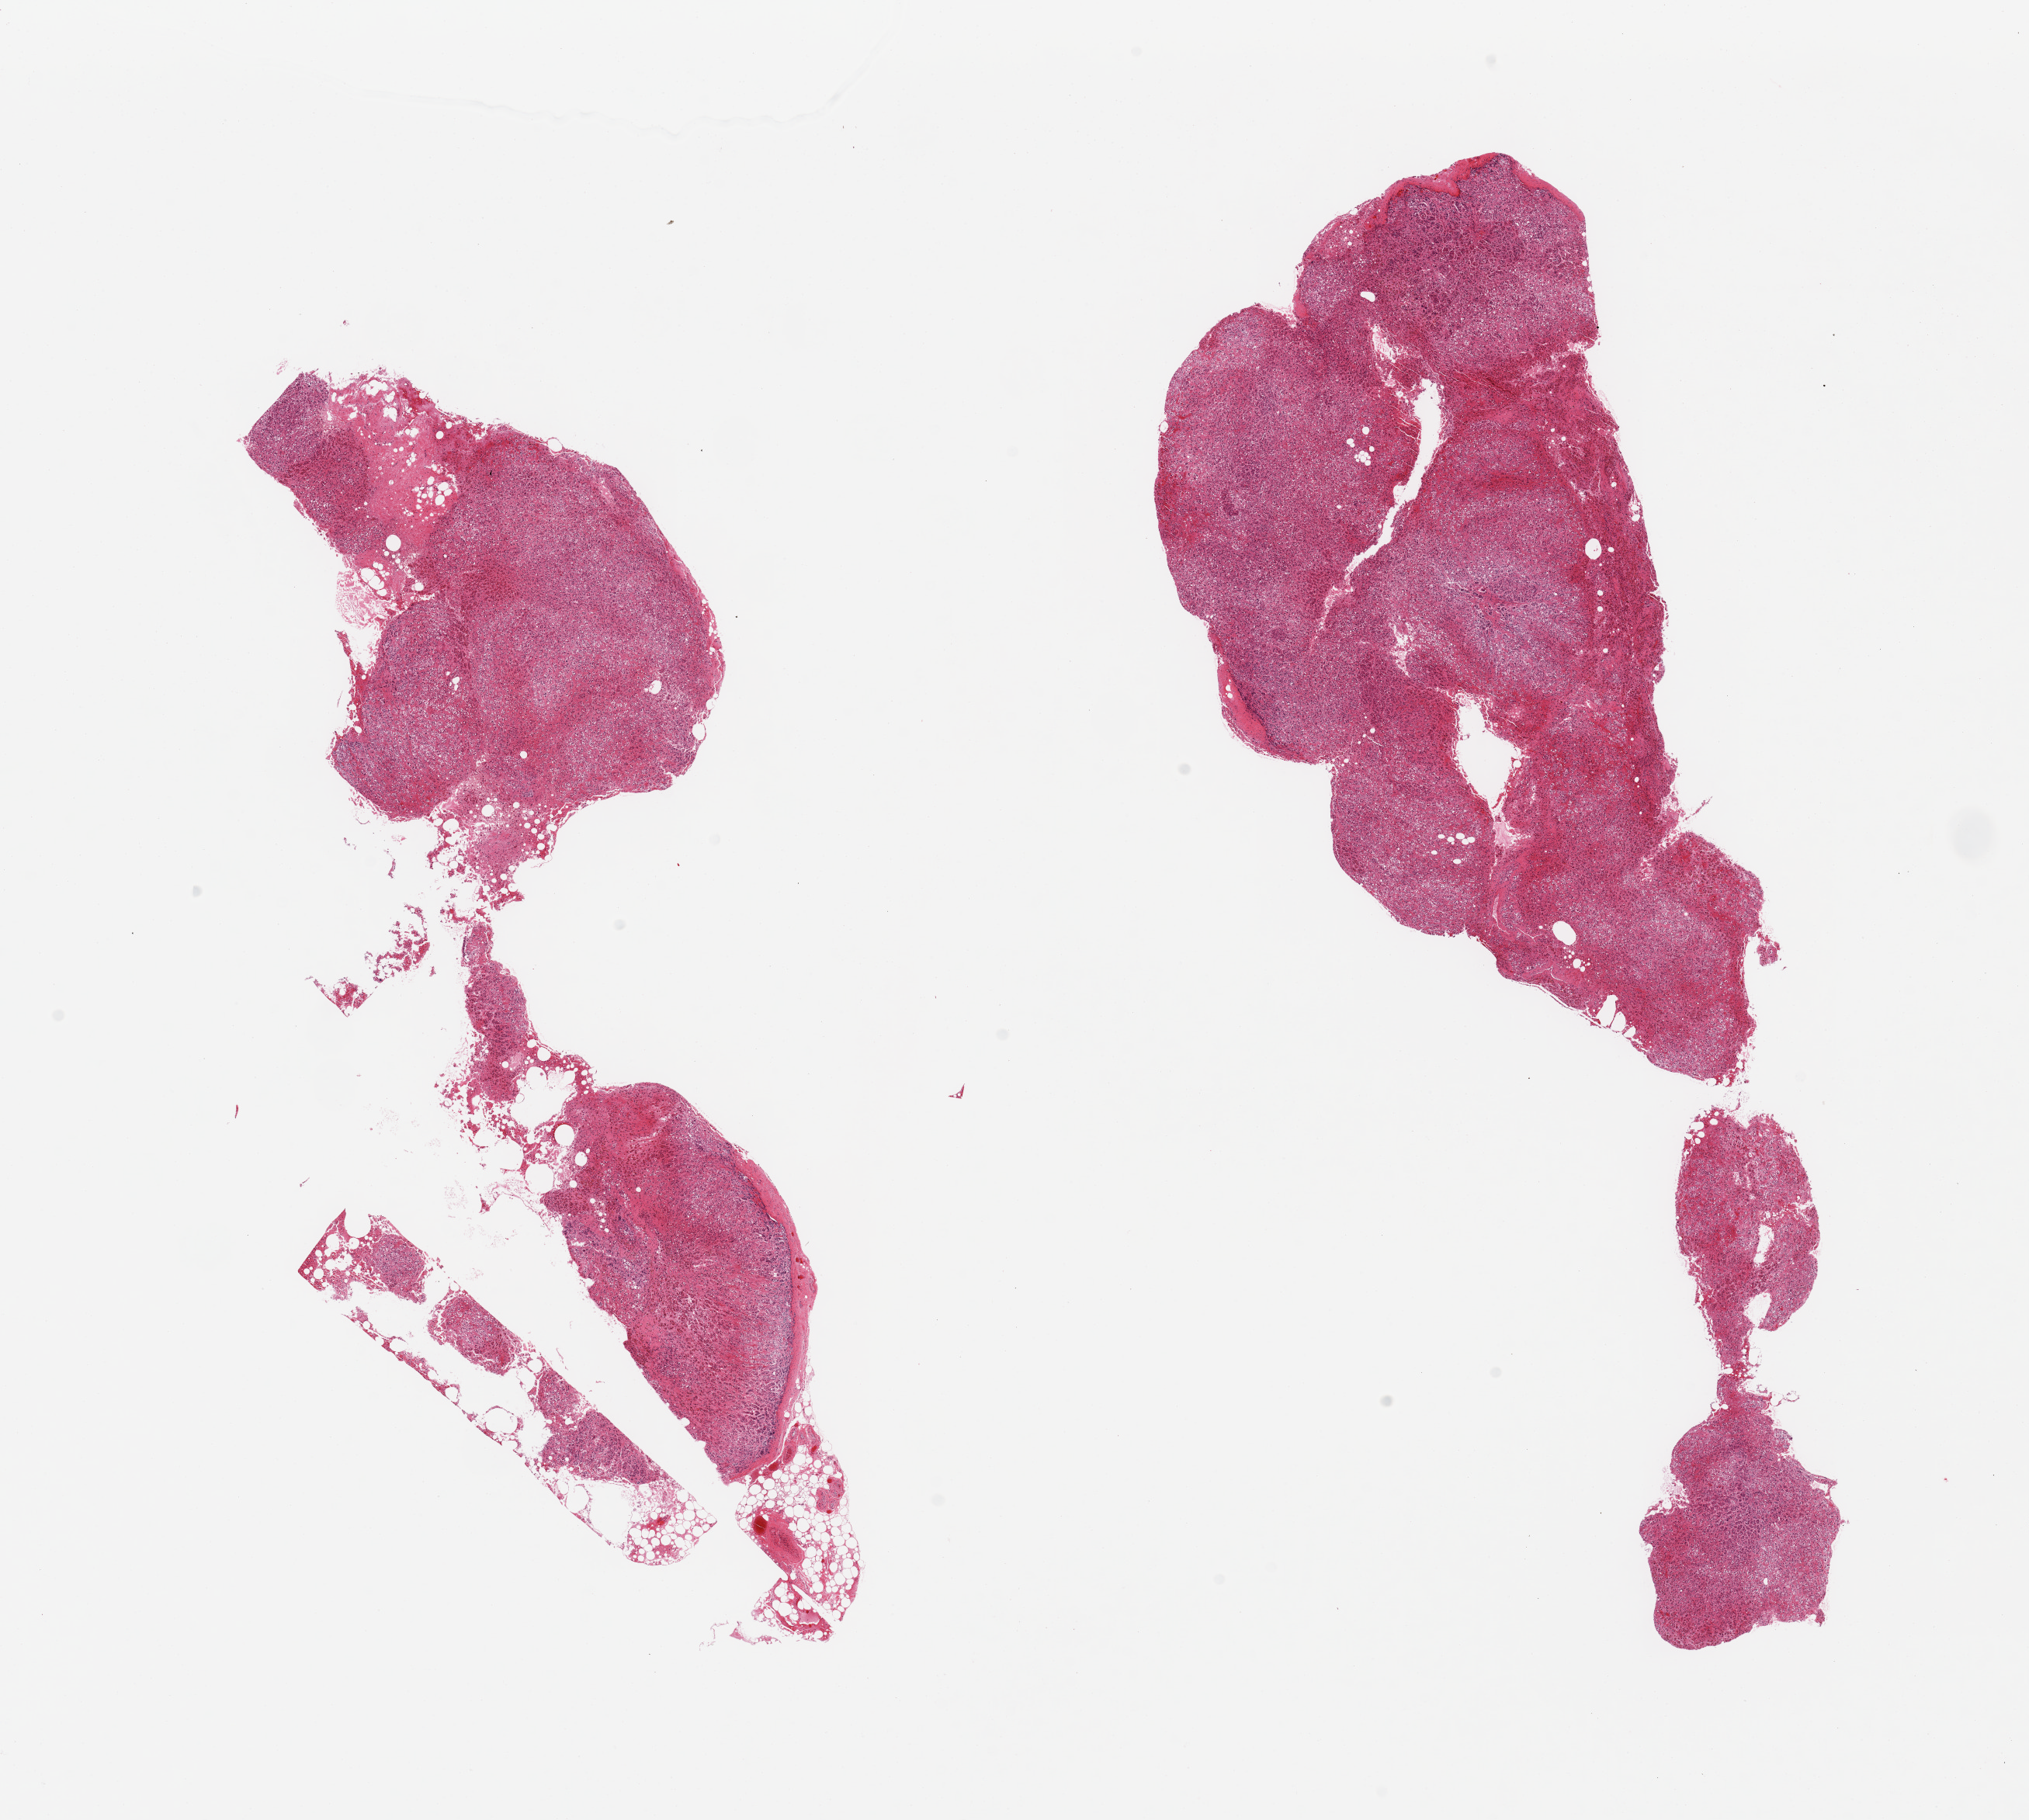
Haematoxylin and eosin whole-slide image, shown as a low-resolution overview of the whole scanned area (about 20.7 x 18.5 mm, from a 20x scan); PAXgene-fixed, paraffin-embedded tissue; sampled site (target tissue): adrenal gland; donor tissue sample. Donor sex: male.
Pathologist's review note for this sample: 2 pieces; minimal attached fat.